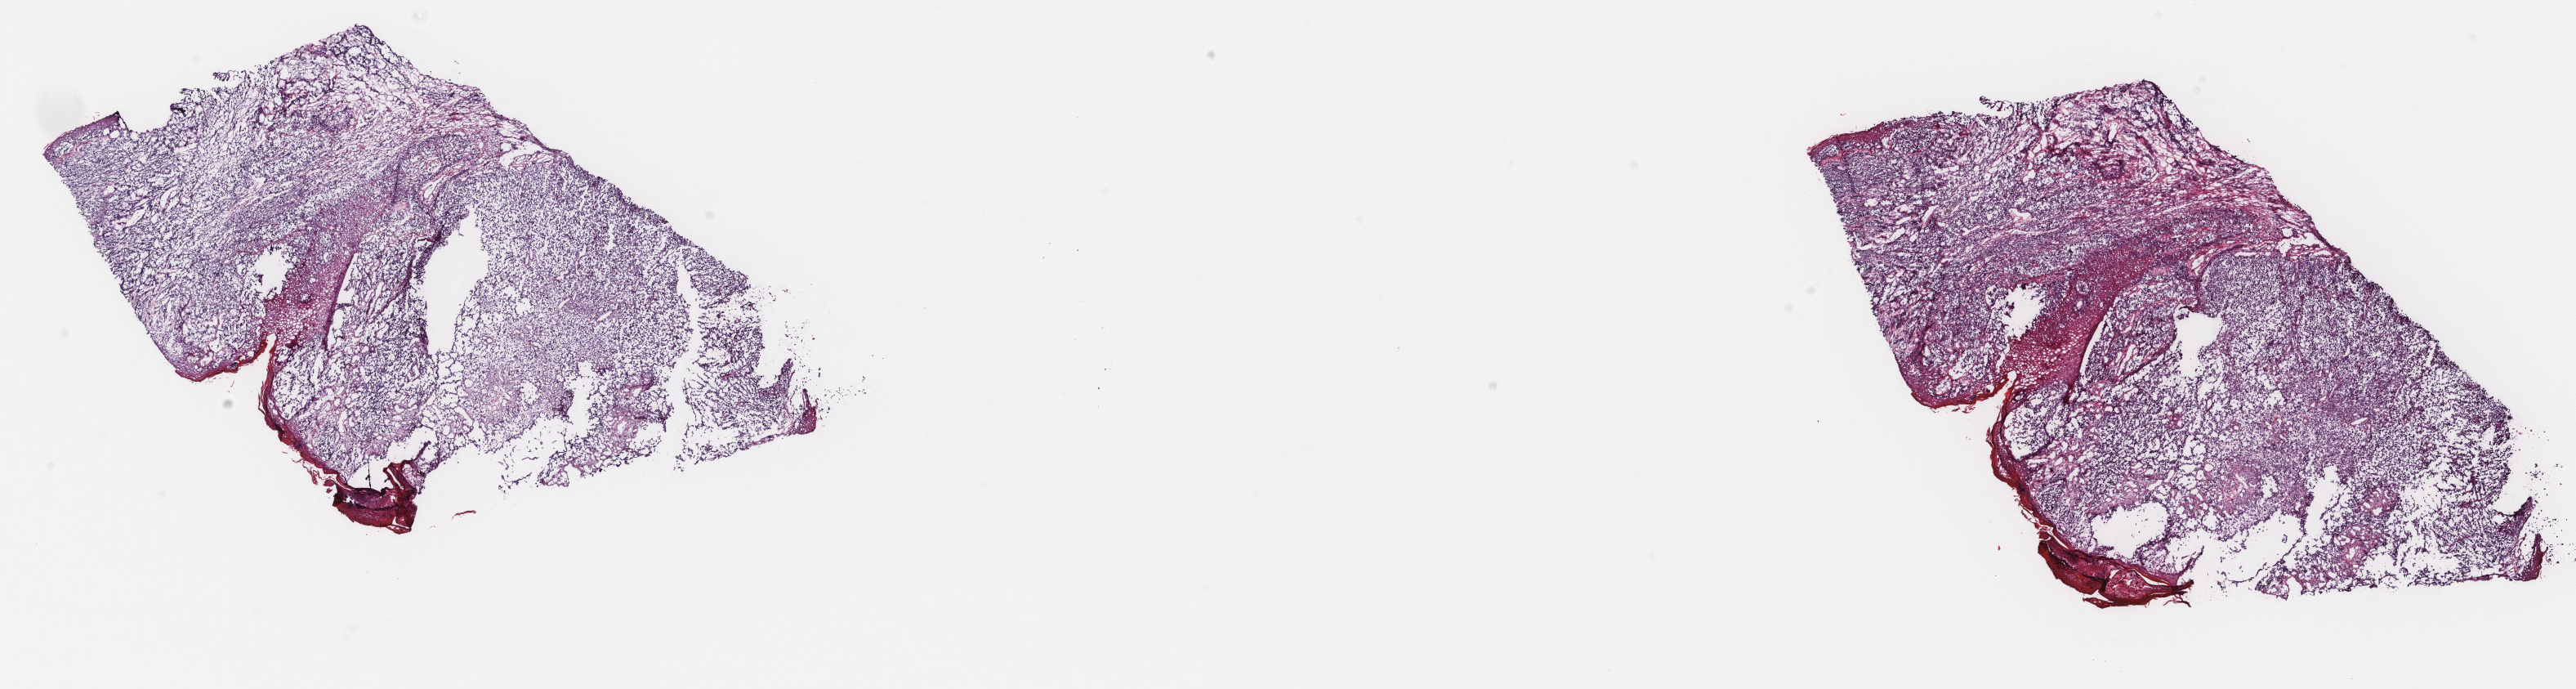
Hematoxylin and eosin (H&E) stained whole-slide image — shown as a low-resolution overview of the whole scanned area (about 25.0 x 6.7 mm, slide scanned at 40x), frozen section from the top of the tissue portion, primary tumour sample from the skin. Male, age 63 years at initial diagnosis. Composition of this section per pathologist review: tumour cells 60%, tumour nuclei 60%, normal cells 15%, stromal cells 25%, necrosis 0%. Inflammatory infiltration, as recorded: lymphocyte infiltration 8%, monocyte infiltration 0%, neutrophil infiltration 0%.
AJCC pathologic stage: IIA (7th edition). Diagnosis: Nodular melanoma.